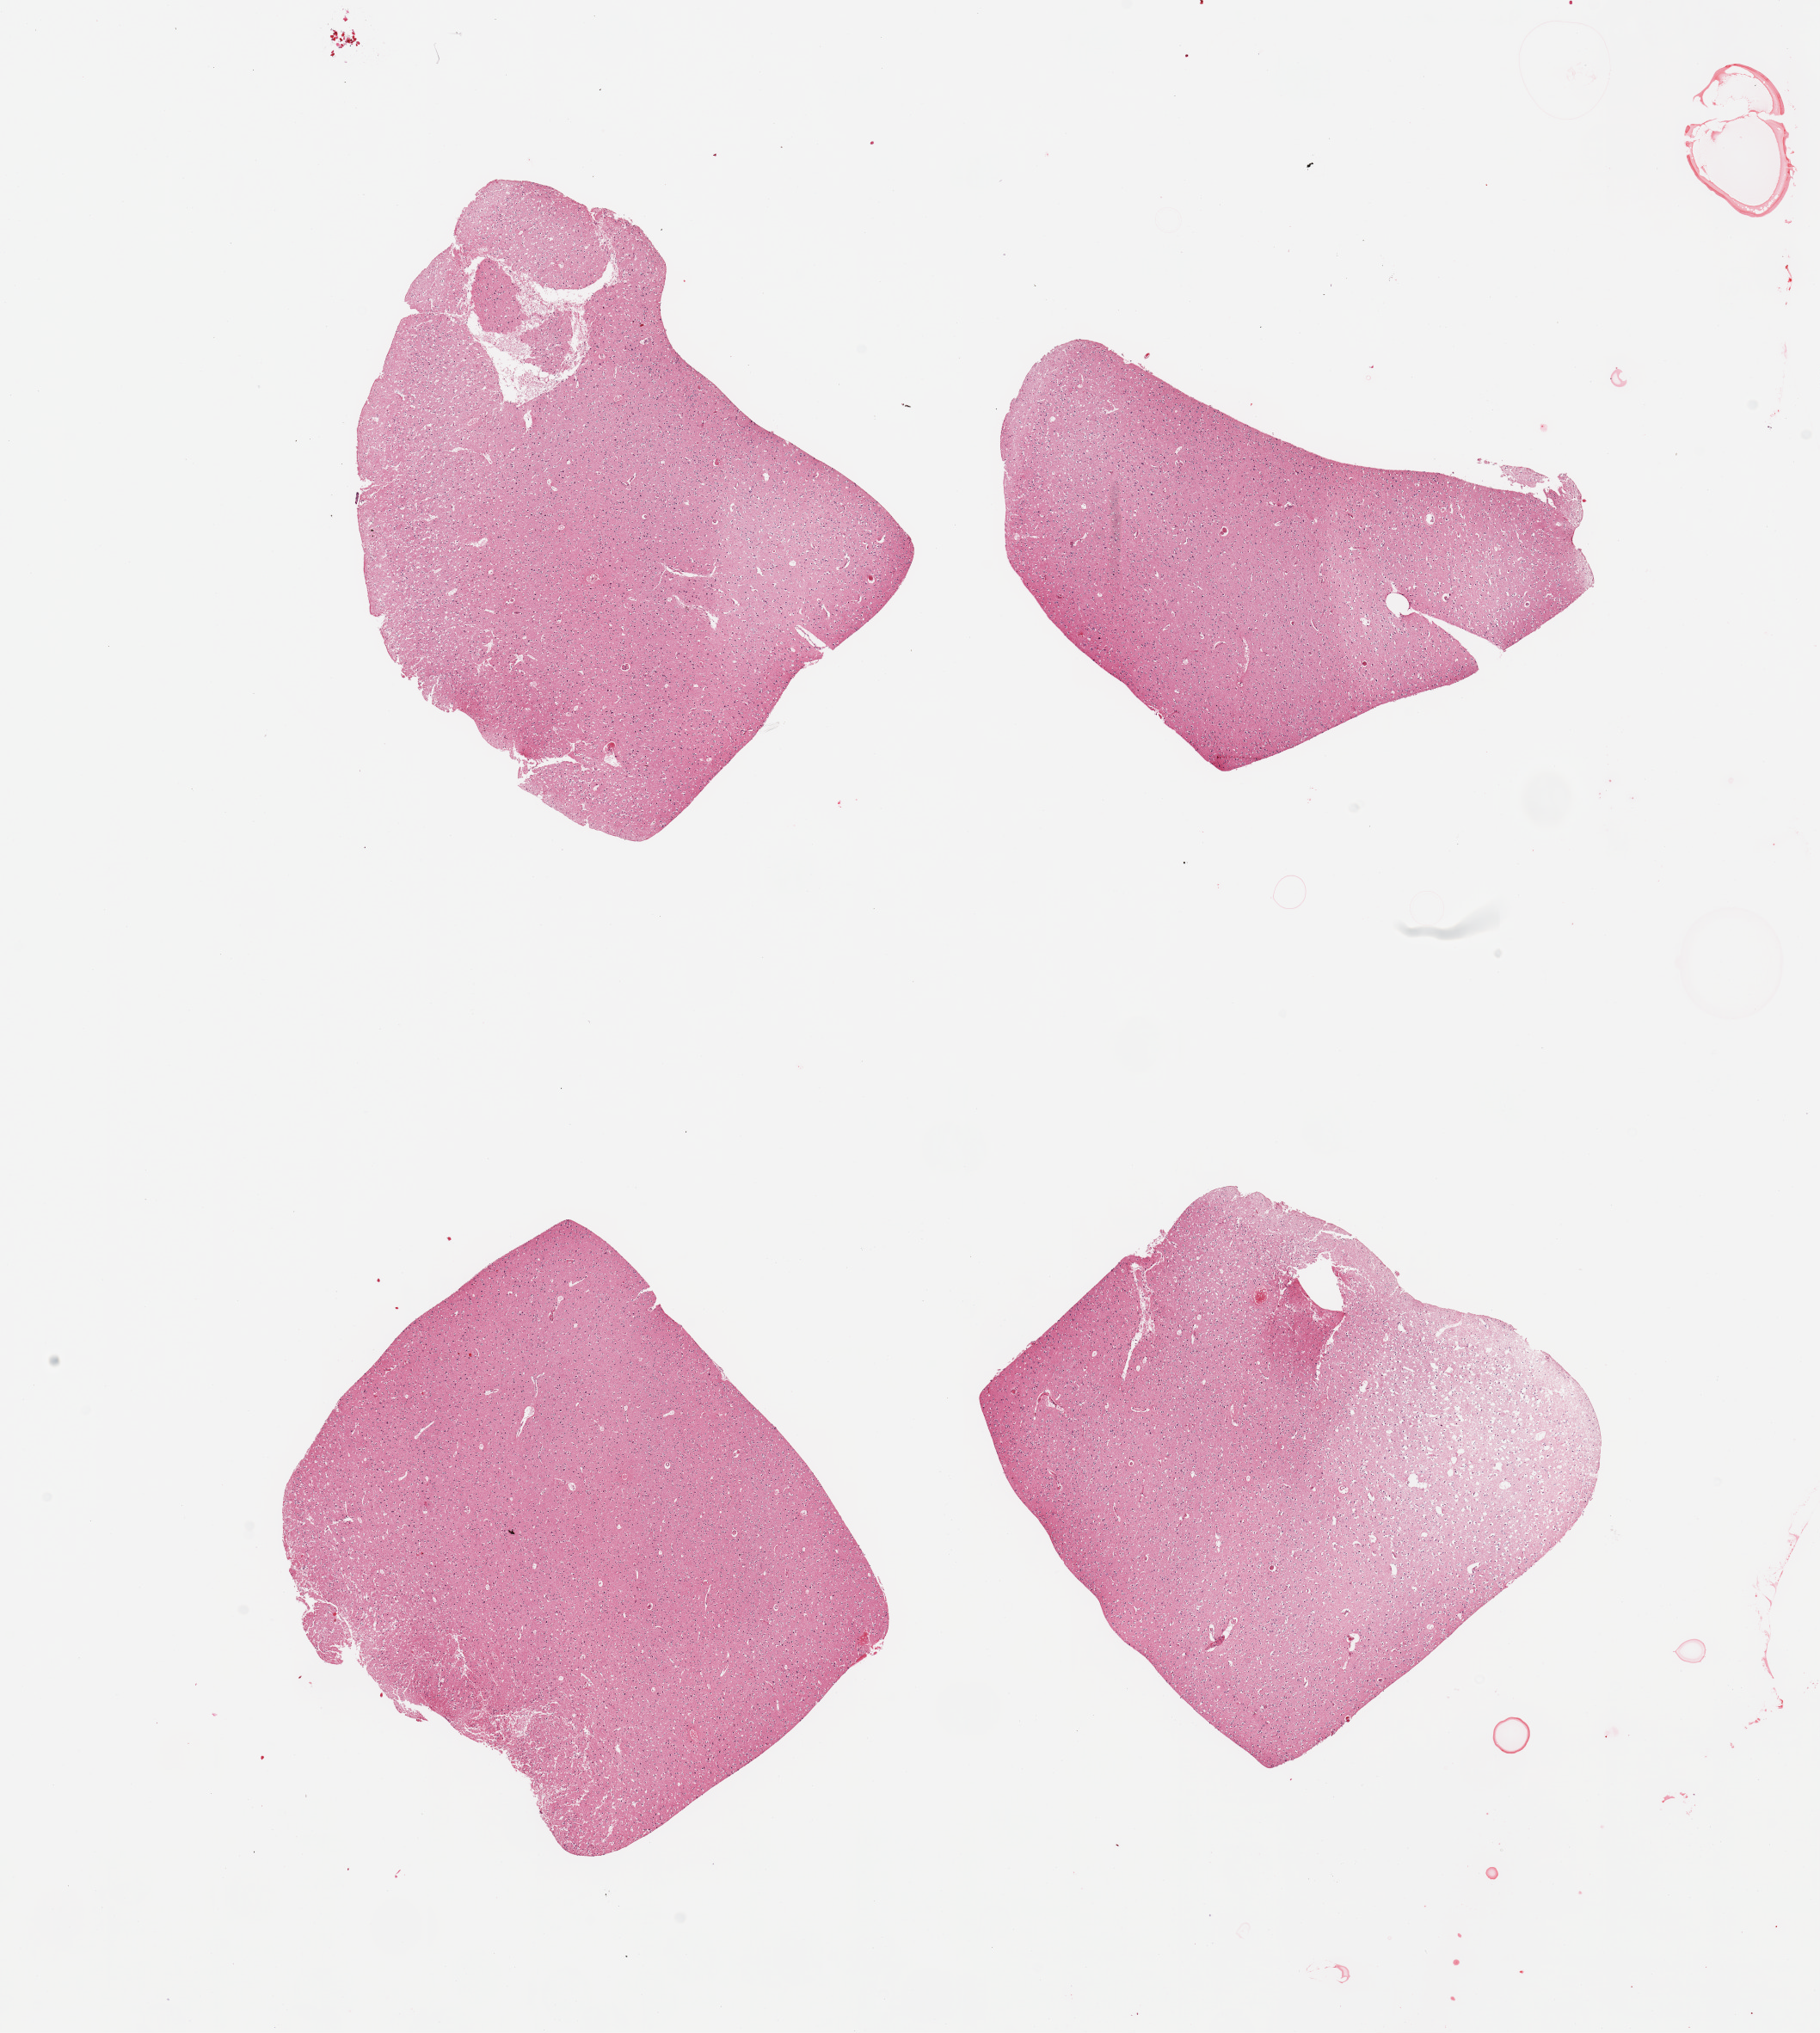
Digitized haematoxylin and eosin-stained section — a low-resolution overview of the entire scanned area, about 16.7 x 18.7 mm (acquisition: 20x scan). PAXgene-fixed paraffin-embedded (PFPE) section. Section of cerebral cortex (target tissue). Donor tissue sample. Donor: female.
- reviewer comment on this tissue sample: 4 pieces